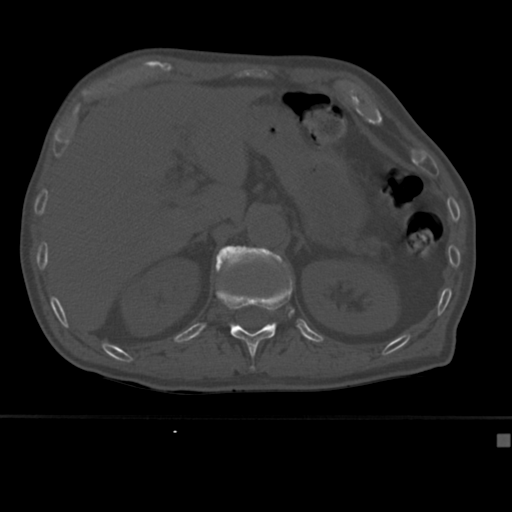
CT including the spine, one axial slice. Slice 186 of 430 in the series (ordered by position). Reconstruction kernel Br40s. Bone window (W 1800 / L 400 HU). 1.5 mm slice thickness. 512 × 512 image matrix, field of view 337 × 337 mm. Patient: male, 64 years. Case-level facts recorded for this patient, not image findings: primary cancer: uterus; vertebrae with lytic lesions (as recorded): T1, T4, T5, T7, L5.
Outlined on this slice (semi-automatically segmented with operator editing):
- L1 vertebra: bounding box <215,245,288,273> (left, top, right, bottom; pixels)
- T12 vertebra: <216,283,293,370>